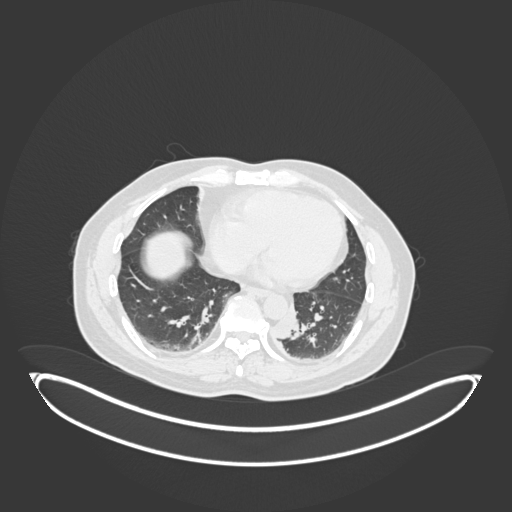
Chest CT, one axial slice; position 56 of 258 along the scan axis; 120 kVp; lung window (W 1500 / L -600 HU); 1 mm slice thickness; 512 × 512 image matrix. Male patient, age 54 years. From the clinical record (not read from this slice): clinical TNM (as recorded): T3 N0 M0.
Annotated regions visible in this slice (rectangle marked by the reading radiologist):
- lung tumour (recorded histology: squamous cell carcinoma): box from (x=273, y=307) to (x=301, y=343) px